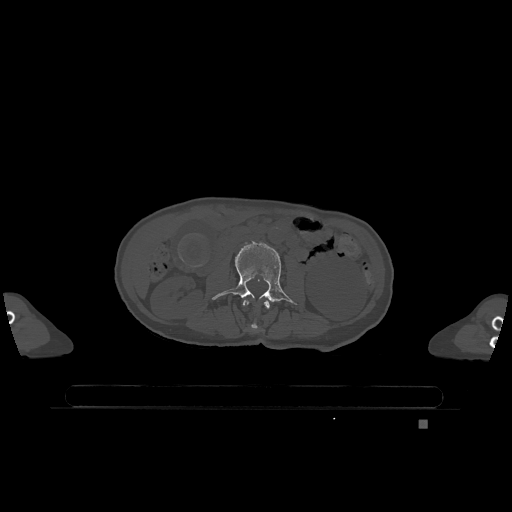
CT including the spine, one axial slice. Position 364 of 1317 along the scan axis. Bone window (W 1800 / L 400 HU). 0.5 mm slice thickness. 512 × 512 image matrix. Female patient, age 74 years. Case-level facts recorded for this patient, not image findings: primary cancer: lung; vertebrae with lytic lesions (as recorded): T1, T4, T5, T6, L4, L5.
Structures marked on this image (semi-automatic segmentation, software-assisted and operator-edited):
- L2 vertebra: bounding box (x1, y1, x2, y2) in pixels: (243, 300, 270, 330)
- L3 vertebra: (212, 242, 295, 304)